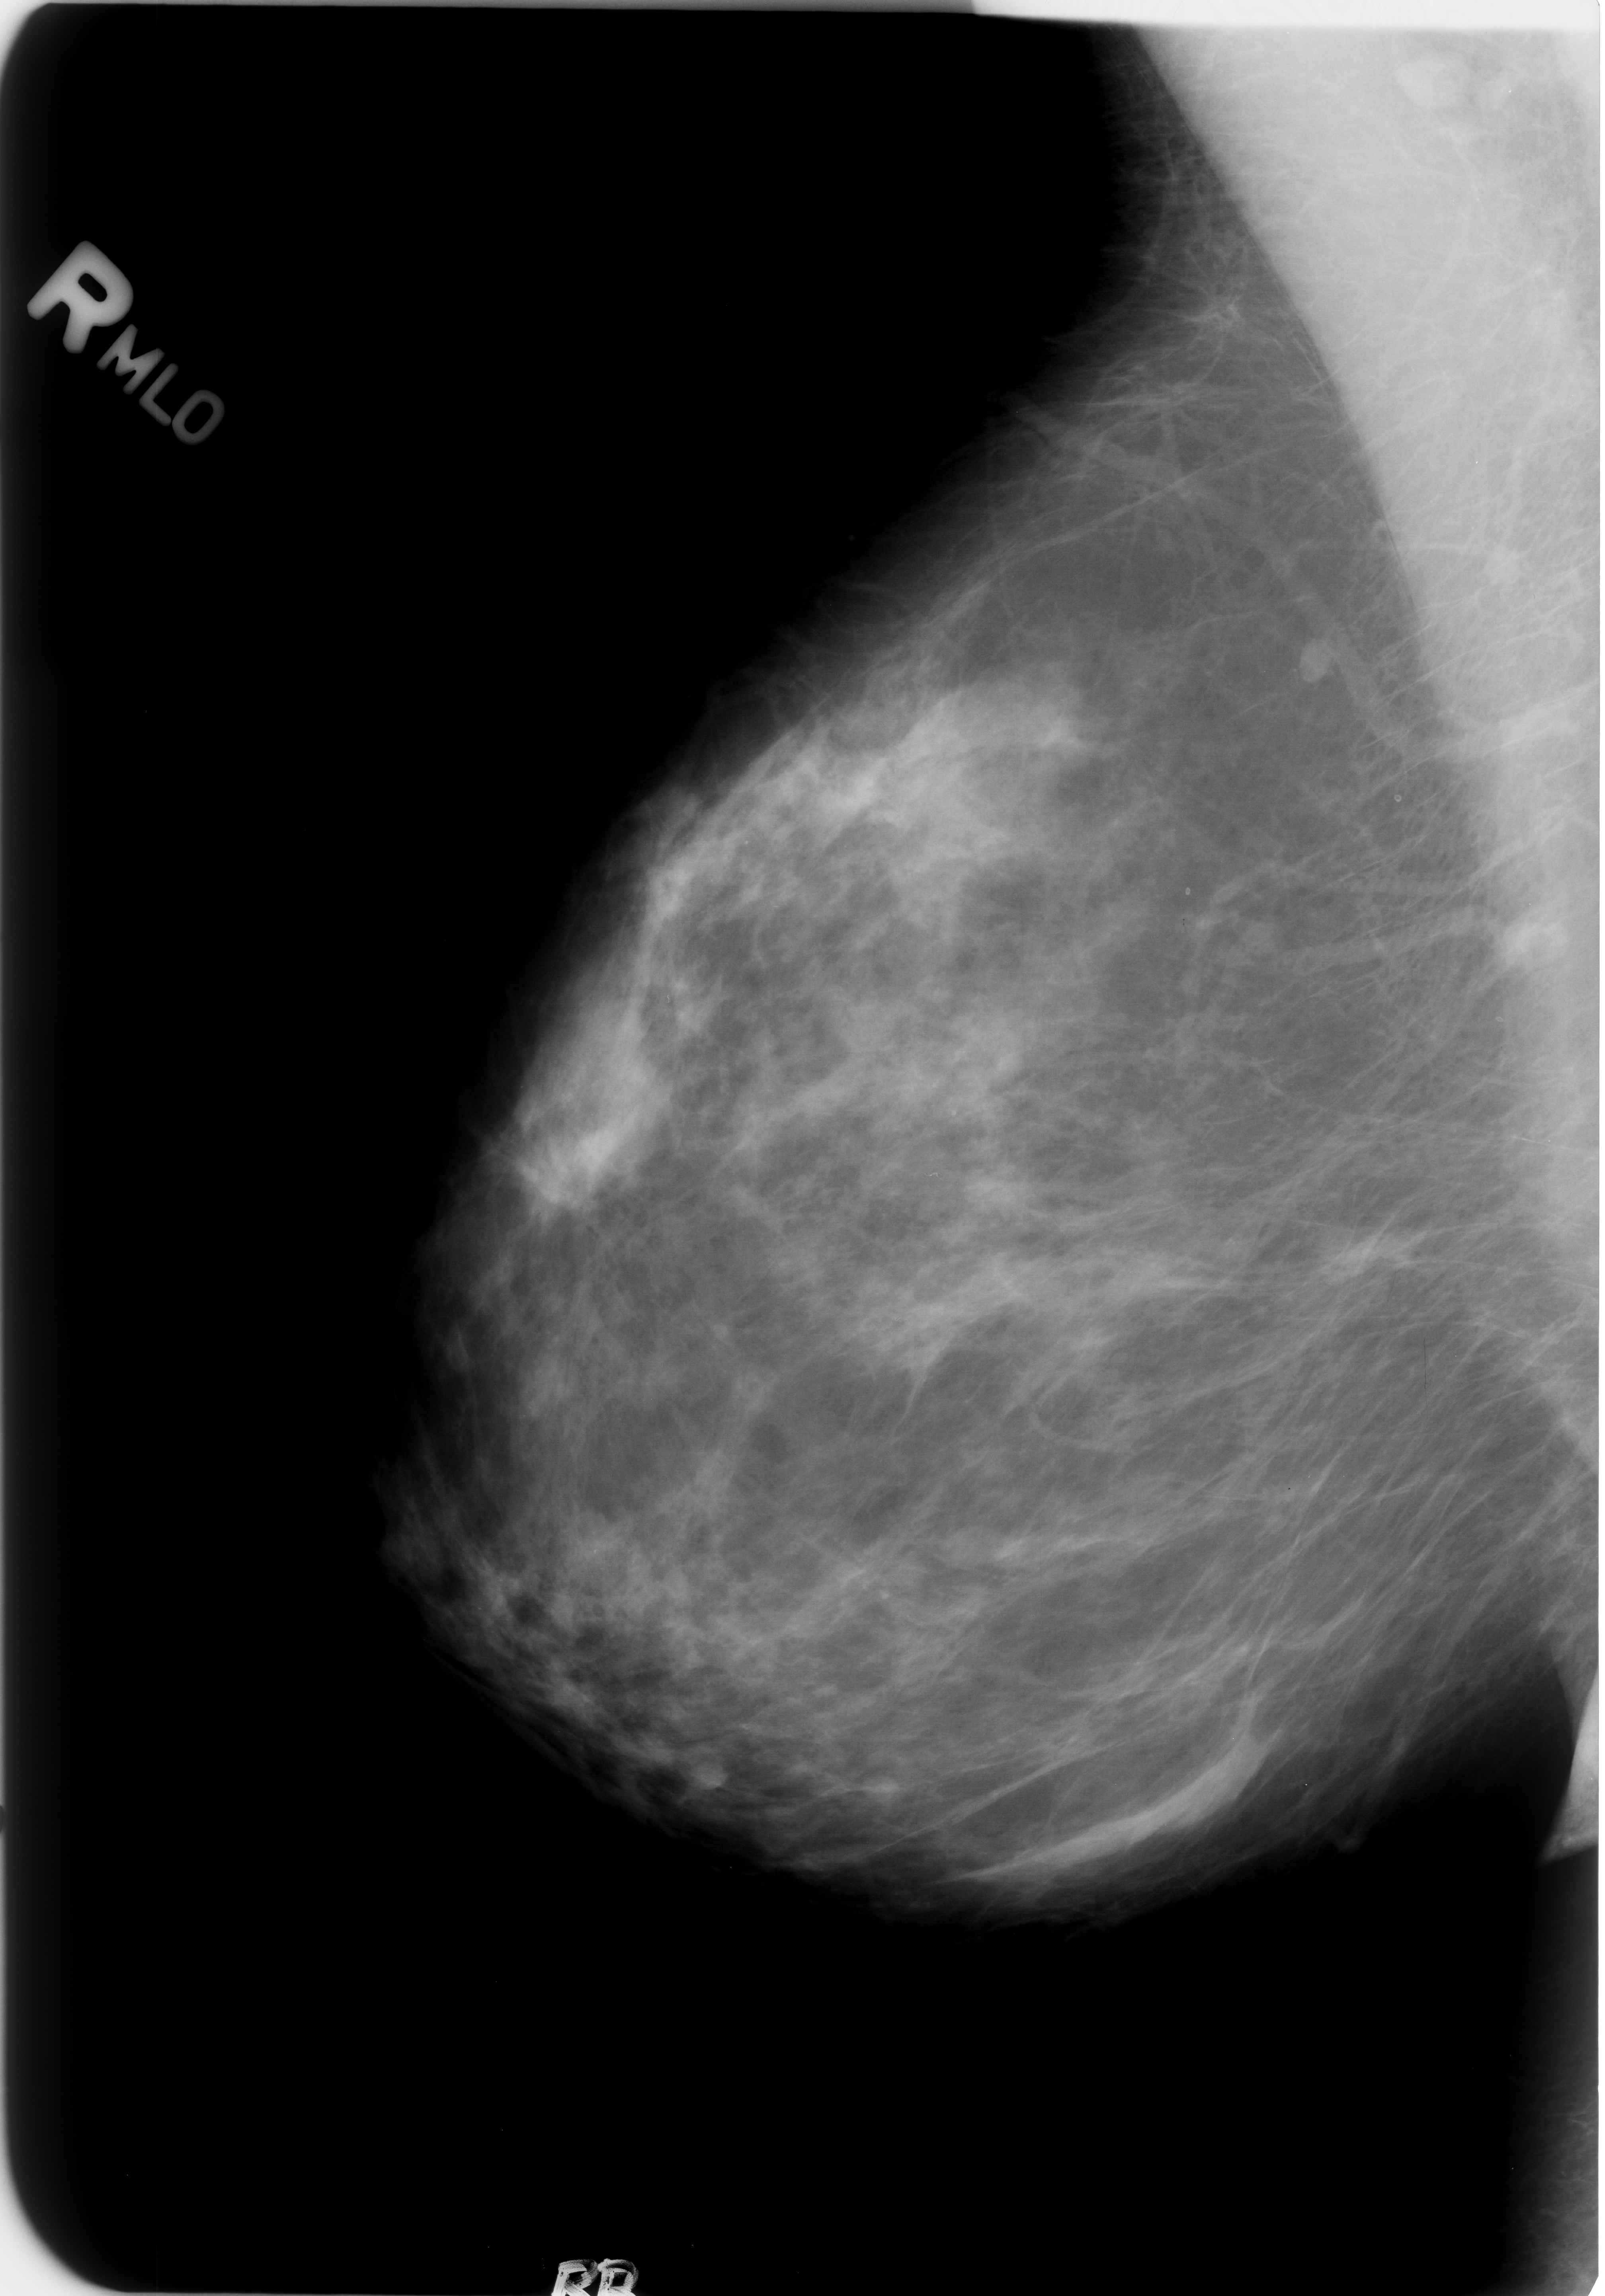
Digitized screen-film mammogram, right breast, MLO view, BI-RADS breast density category 2 (scale 1–4).
- Marked findings (only marked abnormalities are described; nothing is implied about the rest of the image): Finding 1 of 3: calcifications, morphology lucent center; BI-RADS assessment category 2; benign; no additional work-up was recommended (benign without callback).
- Finding 2 of 3: calcifications, morphology lucent center; BI-RADS assessment category 2; benign; no additional work-up was recommended (benign without callback).
- Finding 3 of 3: calcifications, morphology lucent center; BI-RADS assessment category 2; subtlety rating 3 on a 1 (subtle) to 5 (obvious) scale; benign; no additional work-up was recommended (benign without callback).